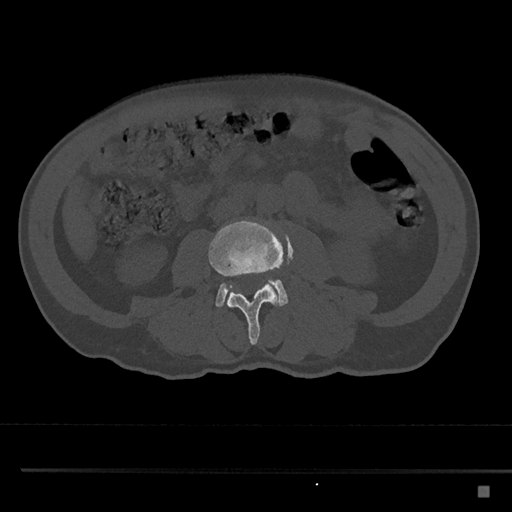
CT including the spine, one axial slice; position 676 of 797 along the scan axis; 120 kVp; bone window (W 1800 / L 400 HU); 0.5 mm slice thickness; 512 × 512 image matrix, field of view 391 × 391 mm. Male patient, age 59 years. From the clinical record (not read from this slice): primary cancer: prostate.
Structures marked on this image (semi-automatically segmented with operator editing):
- L3 vertebra: box from (x=208, y=219) to (x=284, y=345) px
- L4 vertebra: (x=215, y=268)–(x=289, y=308)